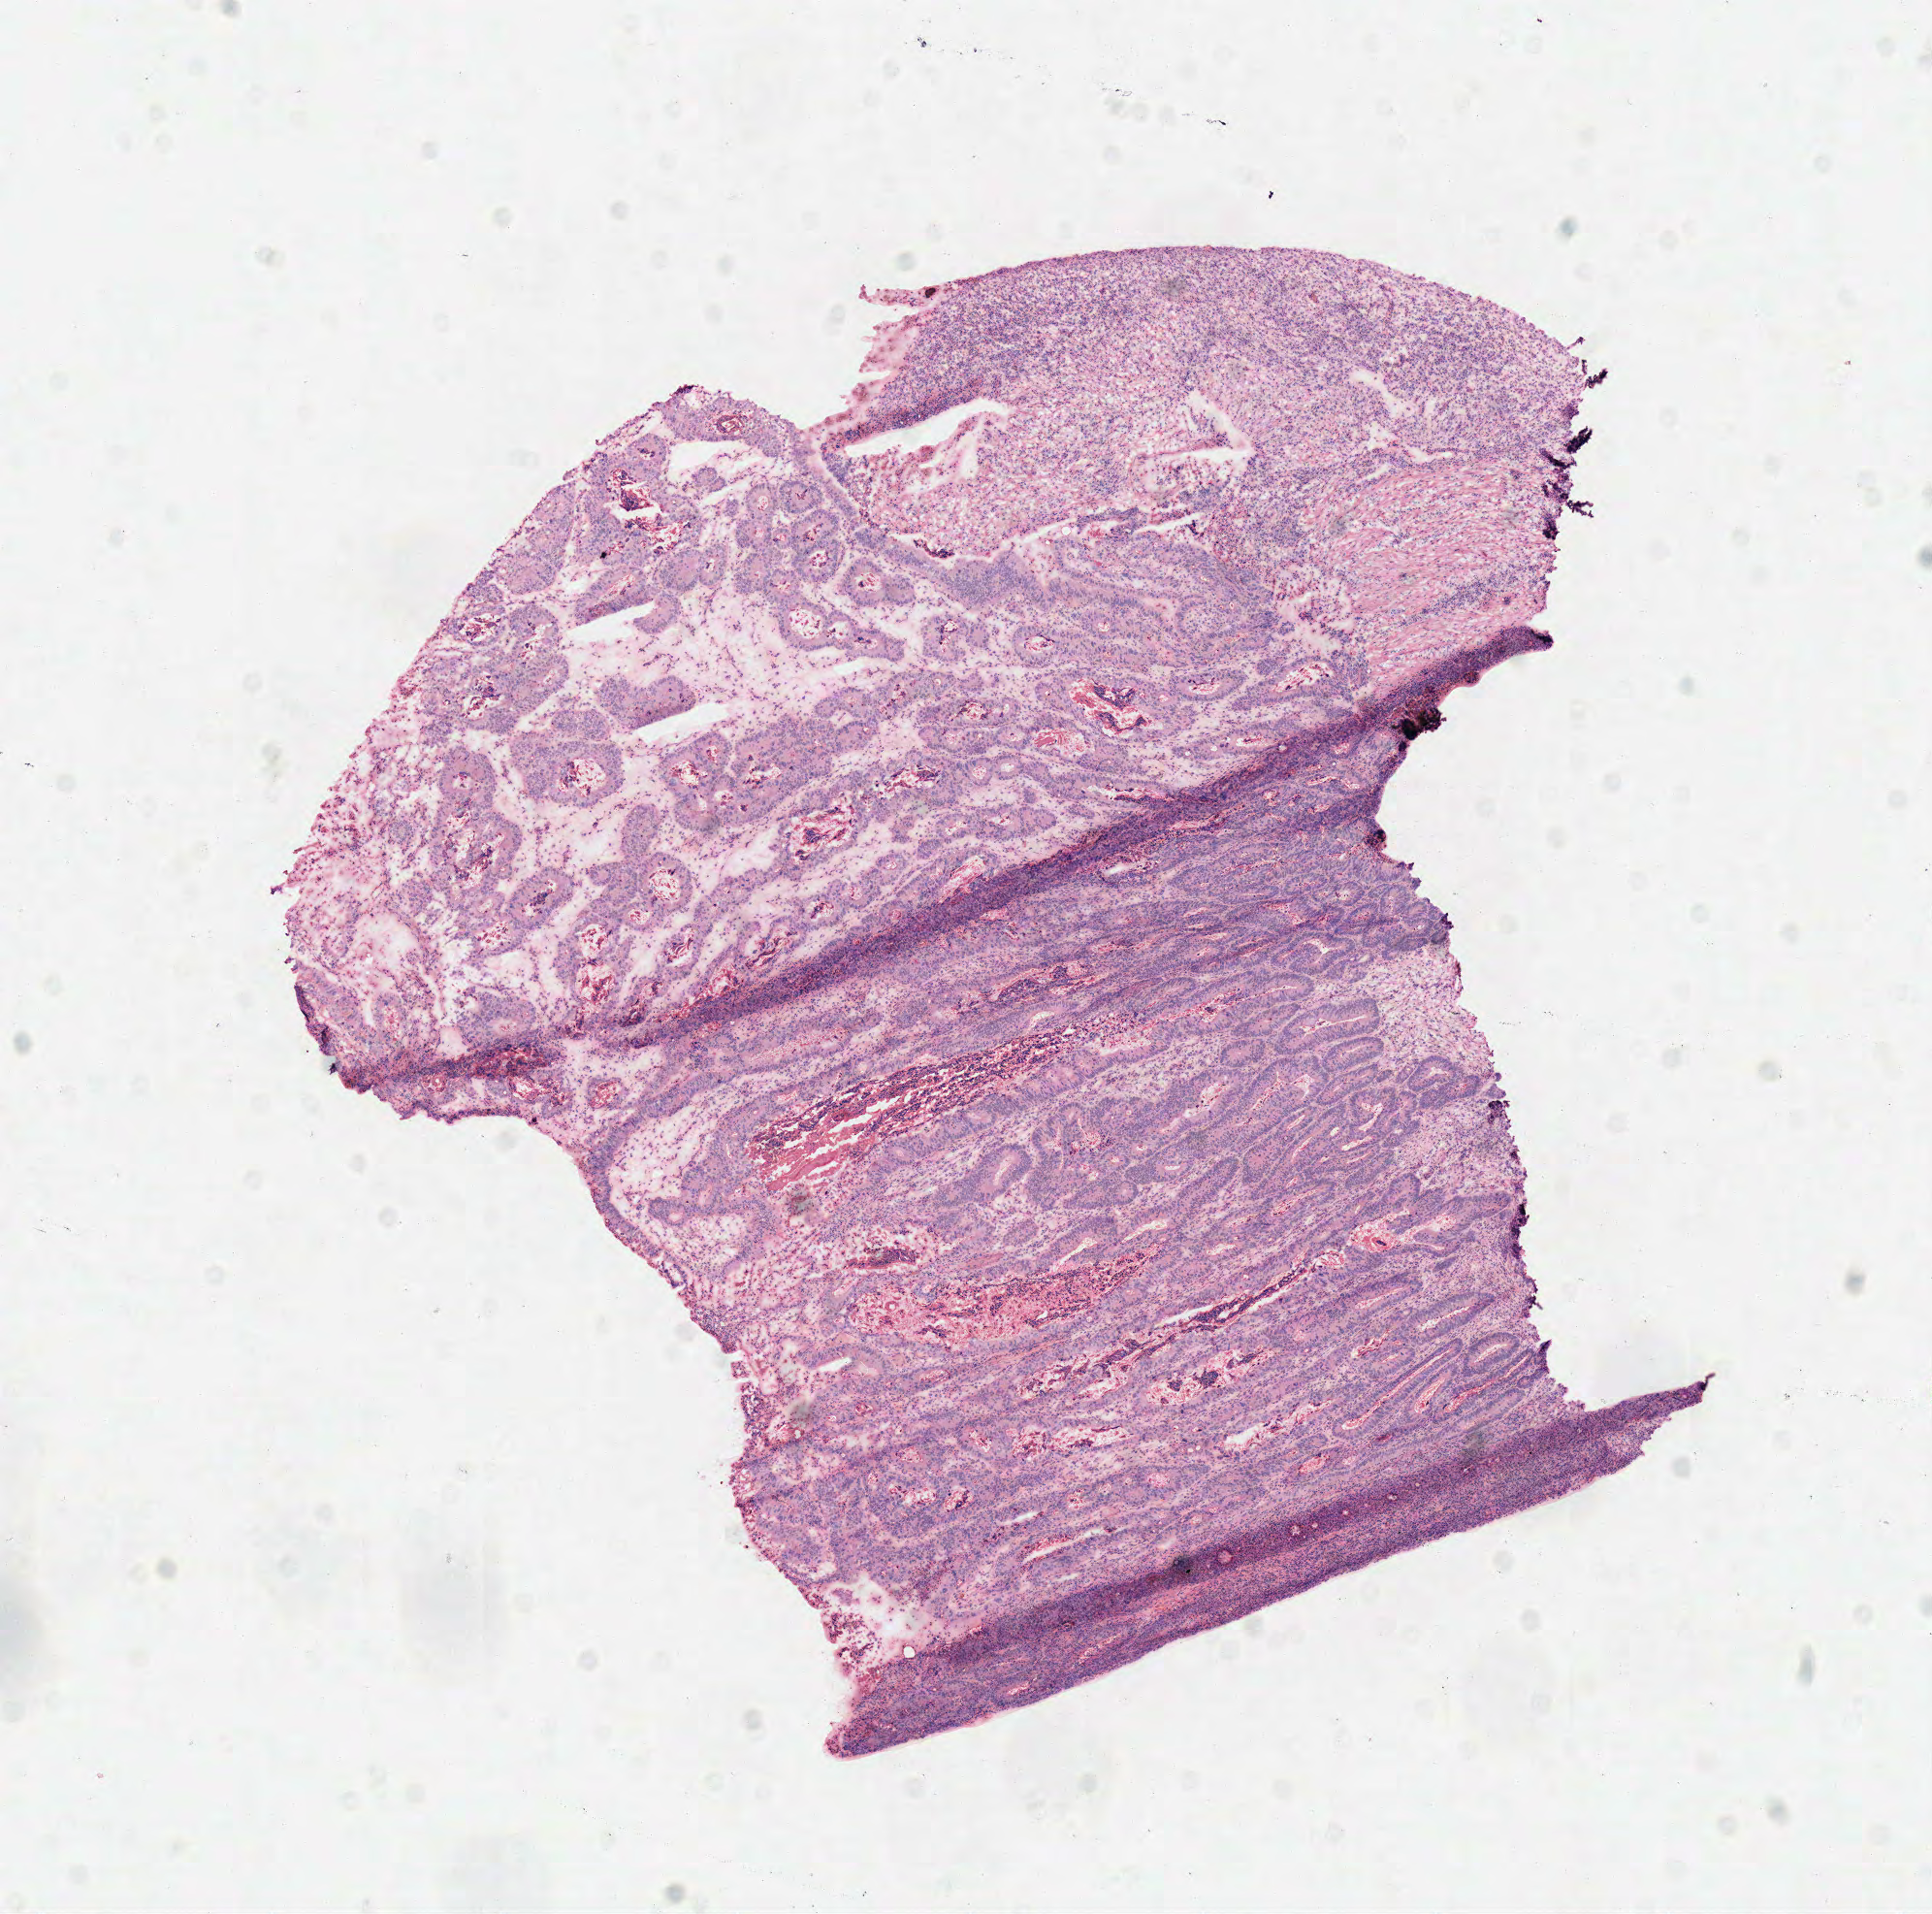
Whole-slide histology image, H&E — shown as a low-resolution overview of the whole scanned area (about 7.8 x 7.8 mm); frozen section; colon, primary tumour sample. Female patient; age at initial diagnosis 68 years. Composition of this section per pathologist review: tumour cells 95%, tumour nuclei 80%, normal cells 0%, stromal cells 0%, necrosis 5%. Inflammatory infiltration, as recorded: lymphocyte infiltration 10%, monocyte infiltration 0%, neutrophil infiltration 2%.
* lymph nodes positive (case pathology): 0 of 8 examined
* diagnosis: Adenocarcinoma, NOS (transverse colon)